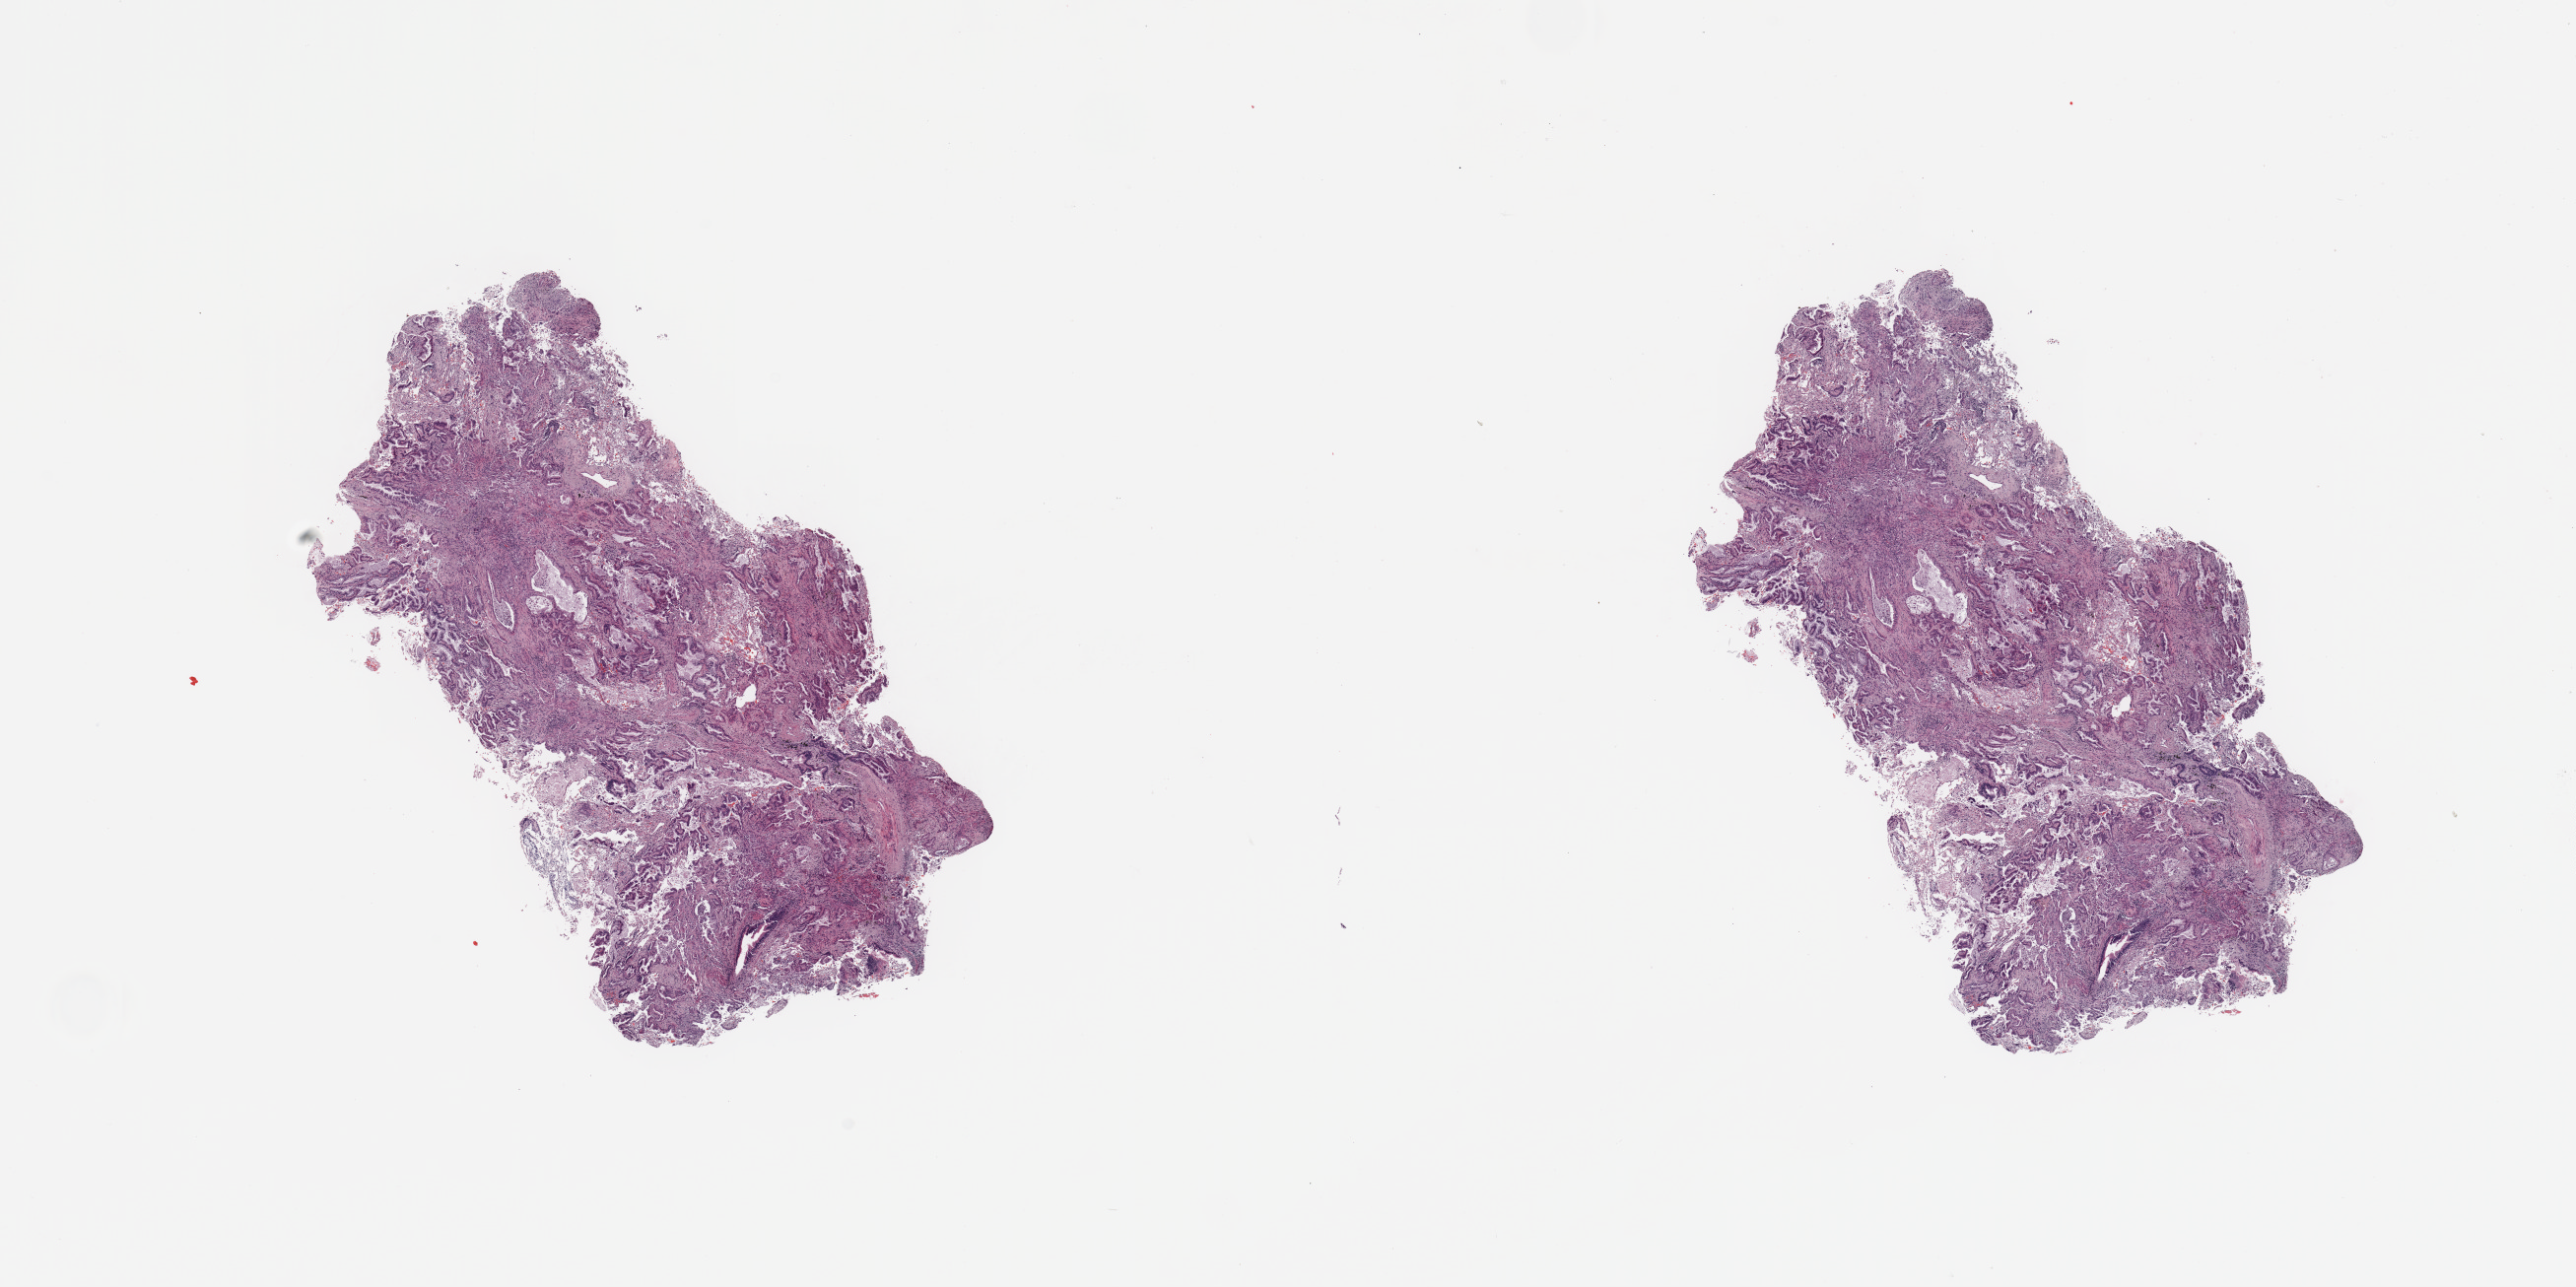
H&E whole-slide image, shown as a low-resolution overview of the whole scanned area (about 20.7 x 10.3 mm, acquisition: 20x scan); tumour tissue sample, lung. Female, 79 y/o. Histologic grade: G1 (well differentiated).
* AJCC pathologic stage: IIB
* diagnosis: Adenocarcinoma, NOS